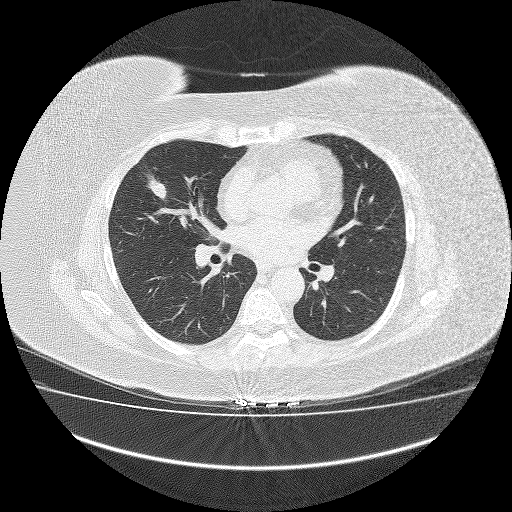
Chest CT (low-dose screening protocol), one axial image, third screening round (two years after baseline), lung window (W 1500 / L -600 HU), 2 mm slice thickness. Female participant, aged 64 years at enrolment. Former smoker at enrolment.
- Lesion marked by an expert reader, bounding box [x1, y1, x2, y2] px = [130, 167, 180, 211].
- Screening reader's record for this exam (one nodule recorded; not confirmed to be the boxed lesion): non-calcified nodule or mass ≥4 mm, right middle lobe, 23 × 13 mm, smooth margins, soft tissue attenuation, pre-existing on the prior screen: no.
- Official screen result: positive, other.
- Lung cancer was diagnosed 31 days after this screen: carcinoid tumor, NOS, right middle lobe, 3 mm at pathology.